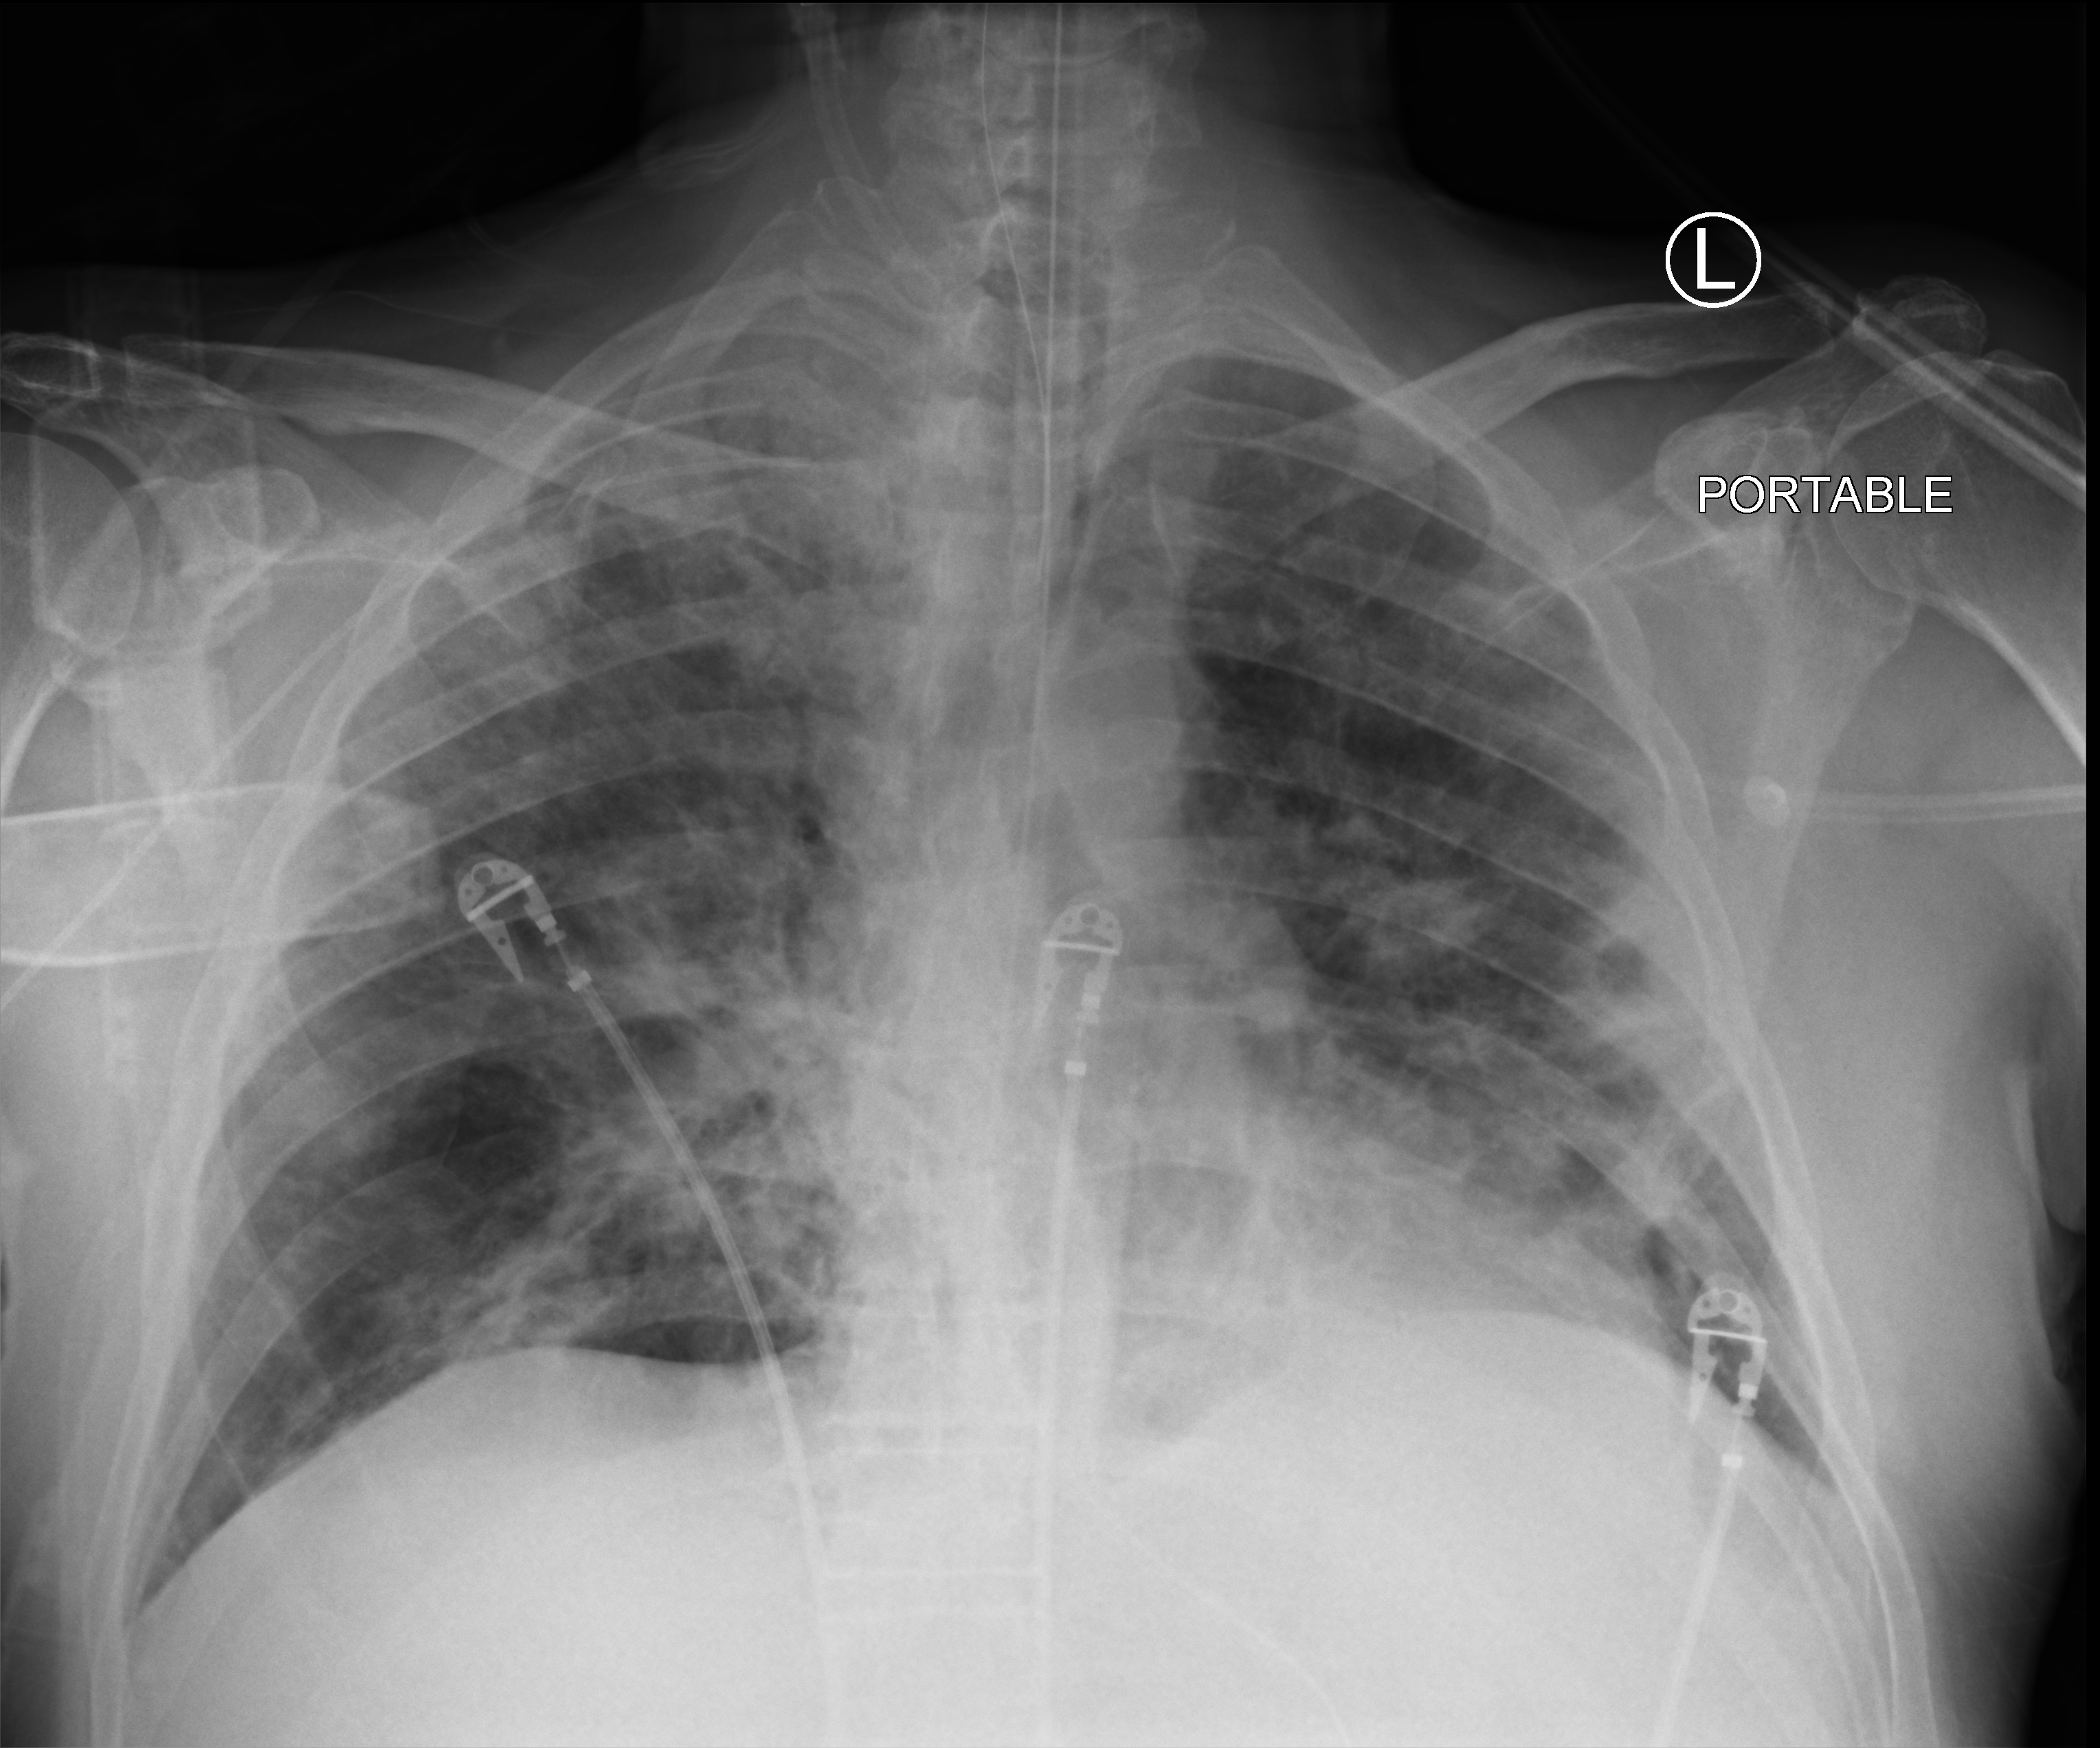
Chest X-ray (portable); anteroposterior (AP) projection. Male patient hospitalised with COVID-19, age 60–74 years.
From the hospital-stay record, not from the radiograph (when in the stay this image was taken is not recorded): admitted to intensive care during this hospital stay: yes.